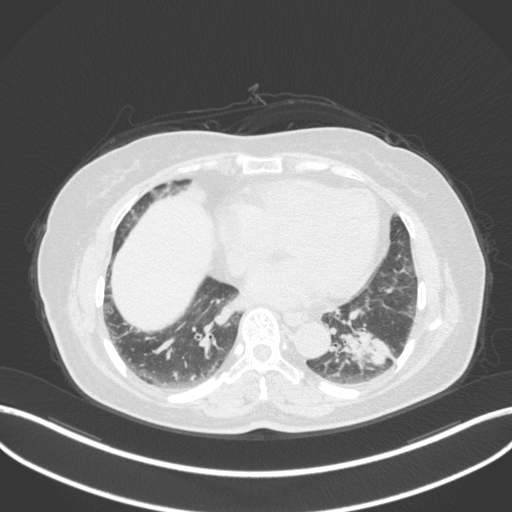
Chest CT, one axial slice. Position 139 of 307 along the scan axis. Reconstruction kernel B31f. 120 kVp. Lung window (W 1500 / L -600 HU). 1 mm slice thickness. 512 × 512 image matrix, field of view 400 × 400 mm. Patient: female, 59 years. From the clinical record (not read from this slice): clinical TNM (as recorded): T2a N0 M0; histopathological grade: G2-3.
Outlined on this slice (rectangle marked by the reading radiologist):
- lung tumour (recorded histology: adenocarcinoma): box from (x=337, y=327) to (x=395, y=374) px